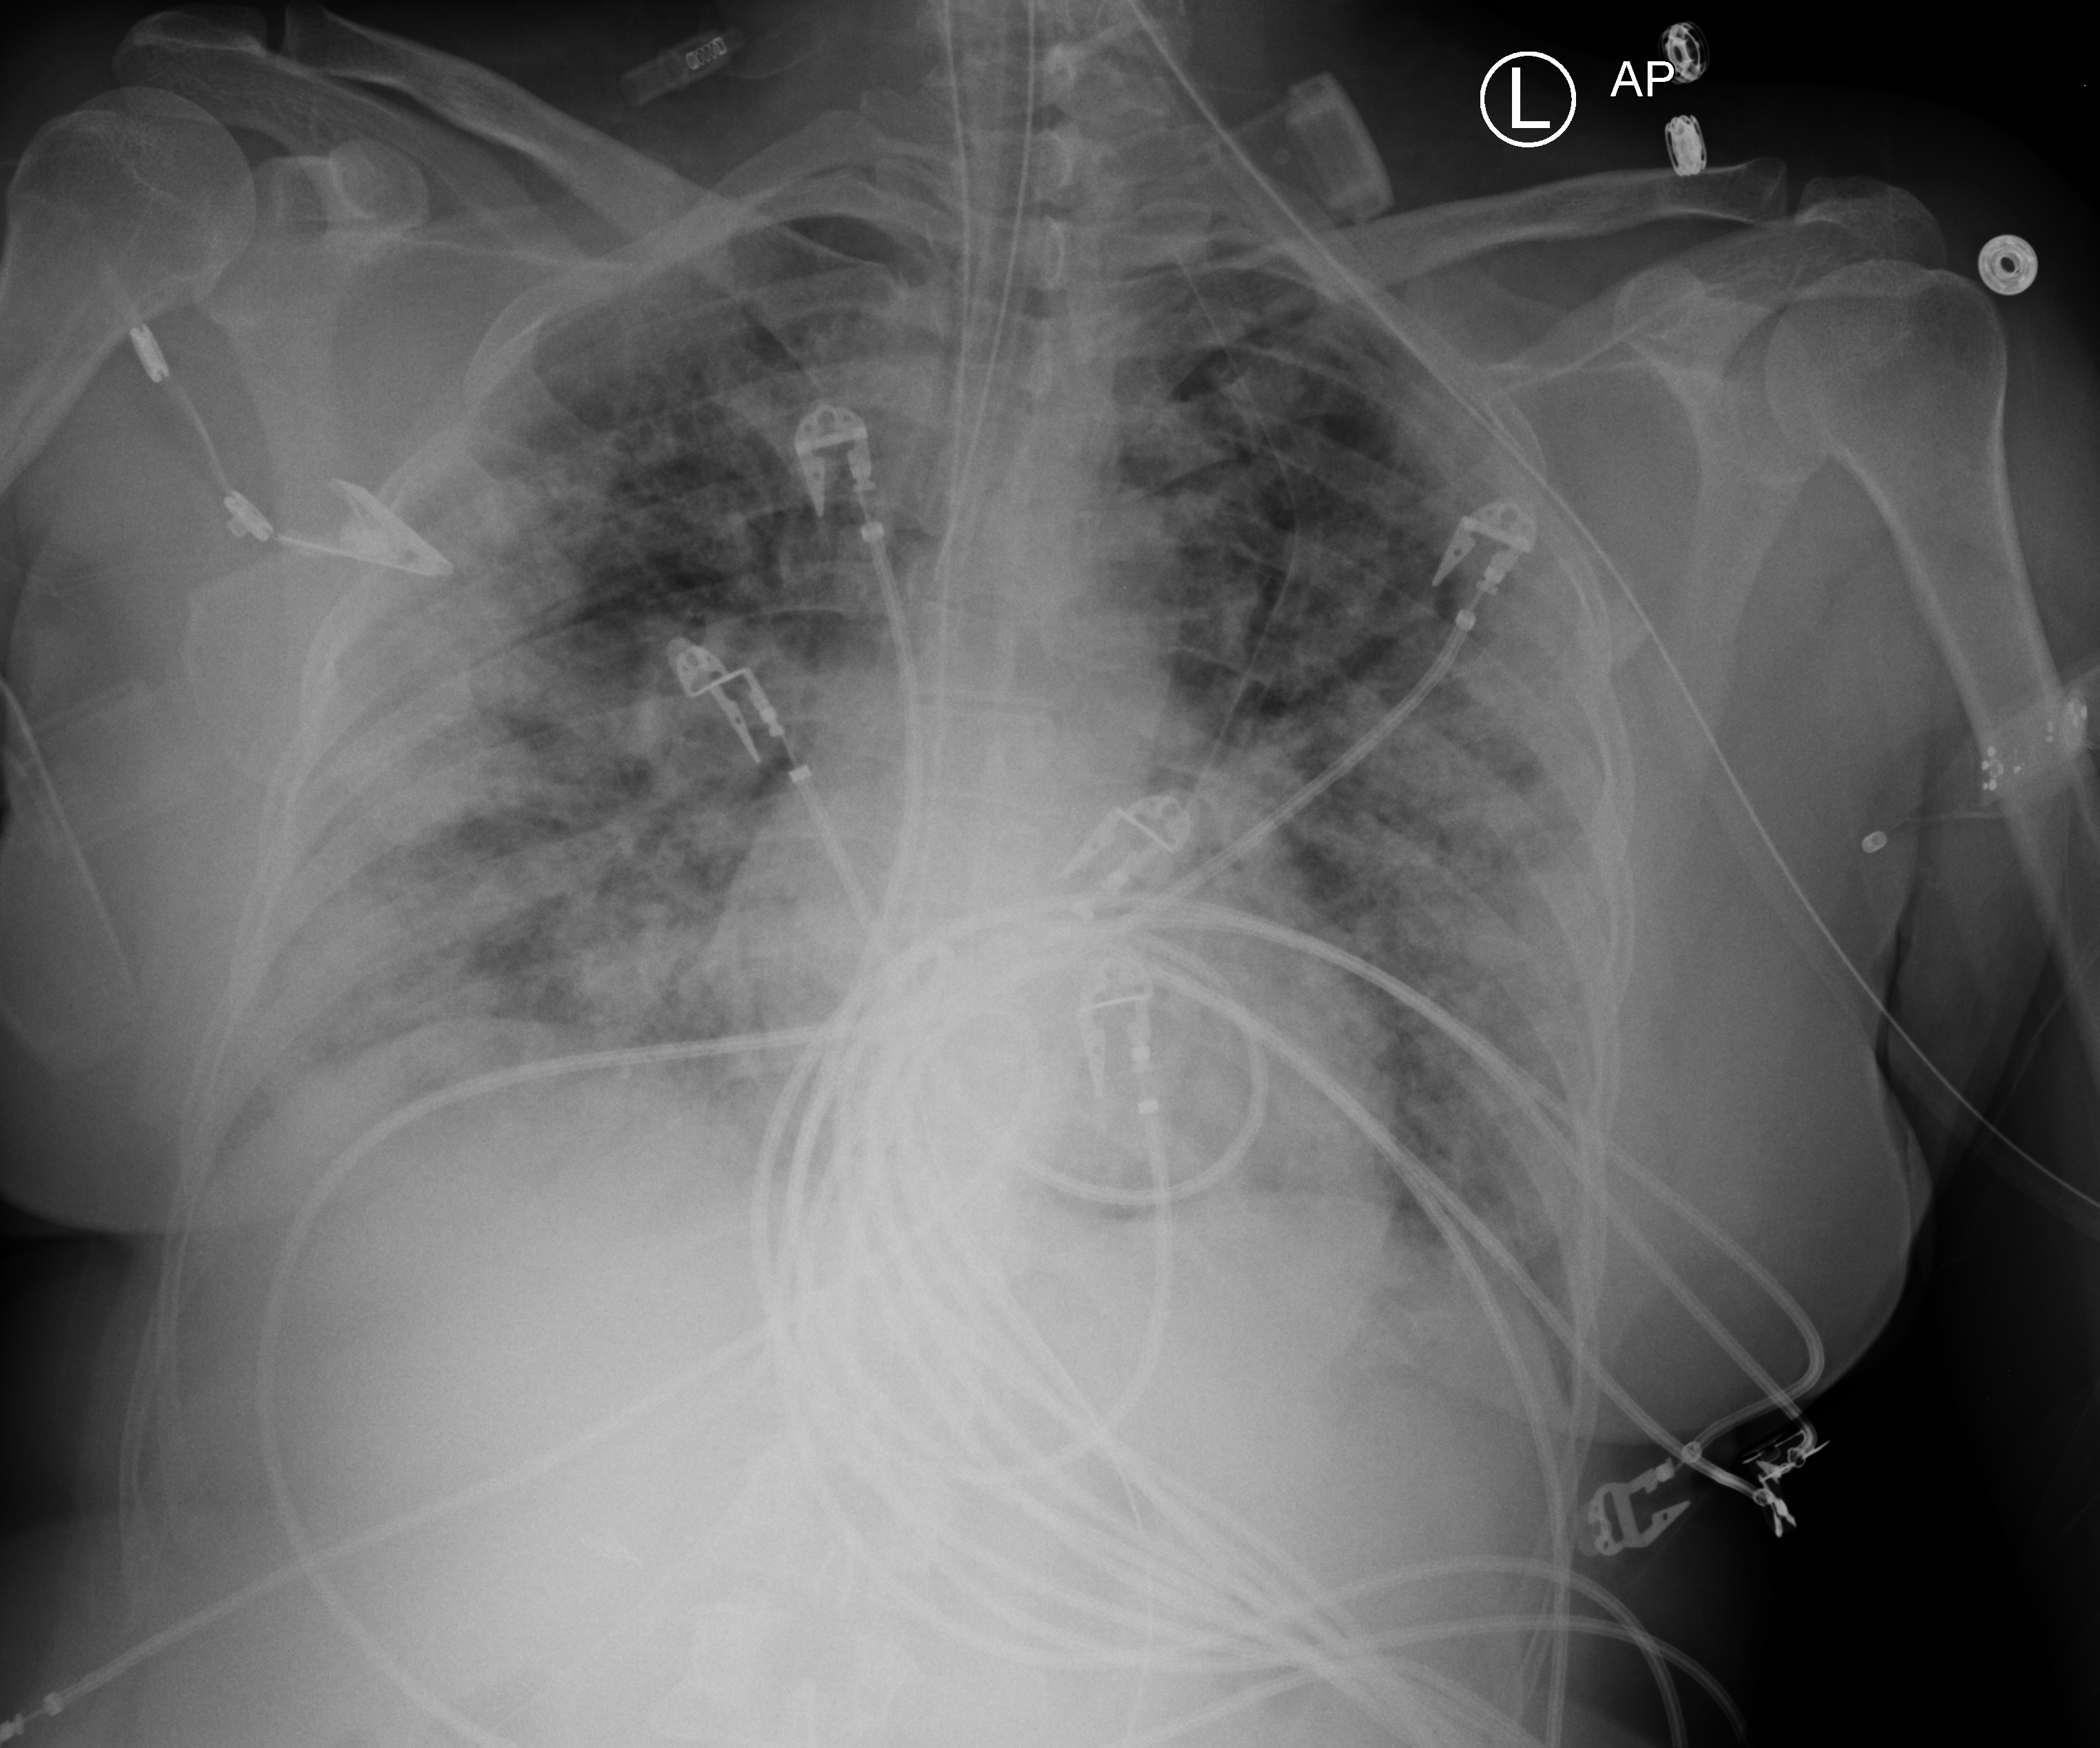
Chest X-ray (portable), anteroposterior (AP) projection. Patient hospitalised with COVID-19; female, aged 18–59 years.
Hospital-stay facts (about this admission, not read from this image; timing relative to this image not recorded):
- admitted to intensive care during this hospital stay: yes
- mechanically ventilated during this hospital stay: yes